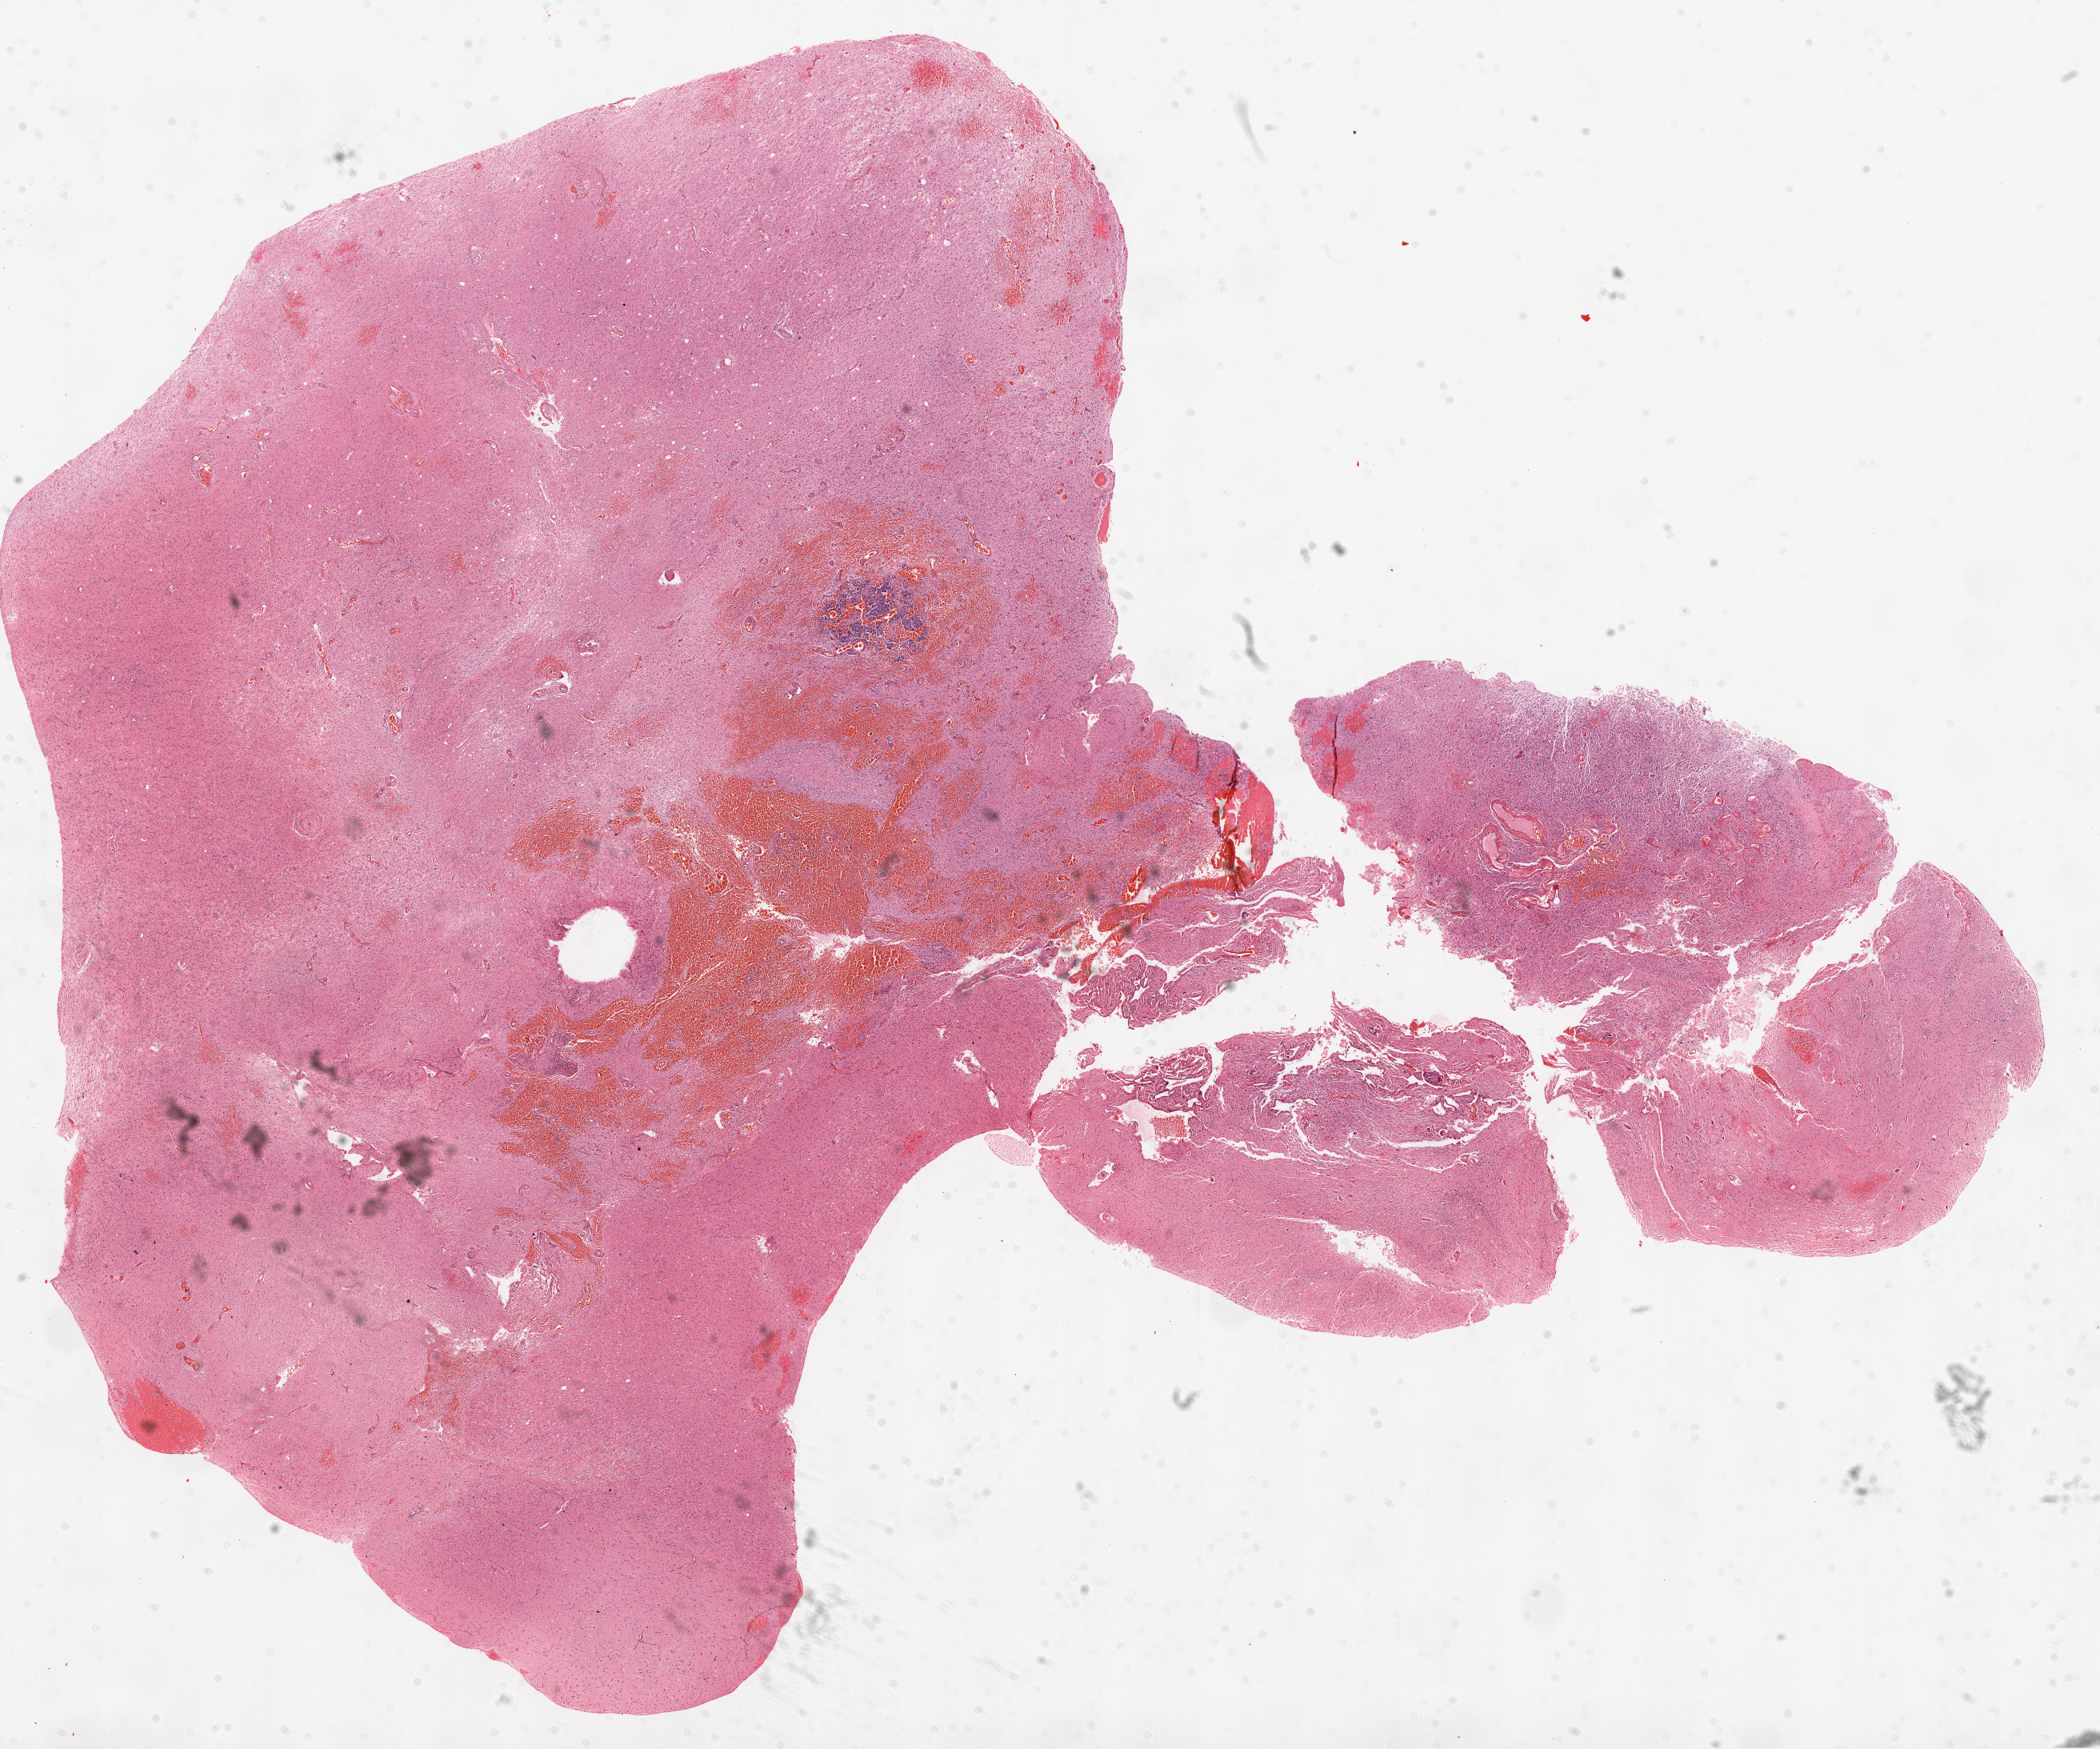
Digitized H&E-stained tissue section (whole slide) — shown as a low-resolution overview of the whole scanned area (about 21.1 x 17.5 mm). Formalin-fixed paraffin-embedded (FFPE) diagnostic section. Sample: primary tumour, brain. Patient: female, age at initial diagnosis 56 years.
• histologic diagnosis: Glioblastoma